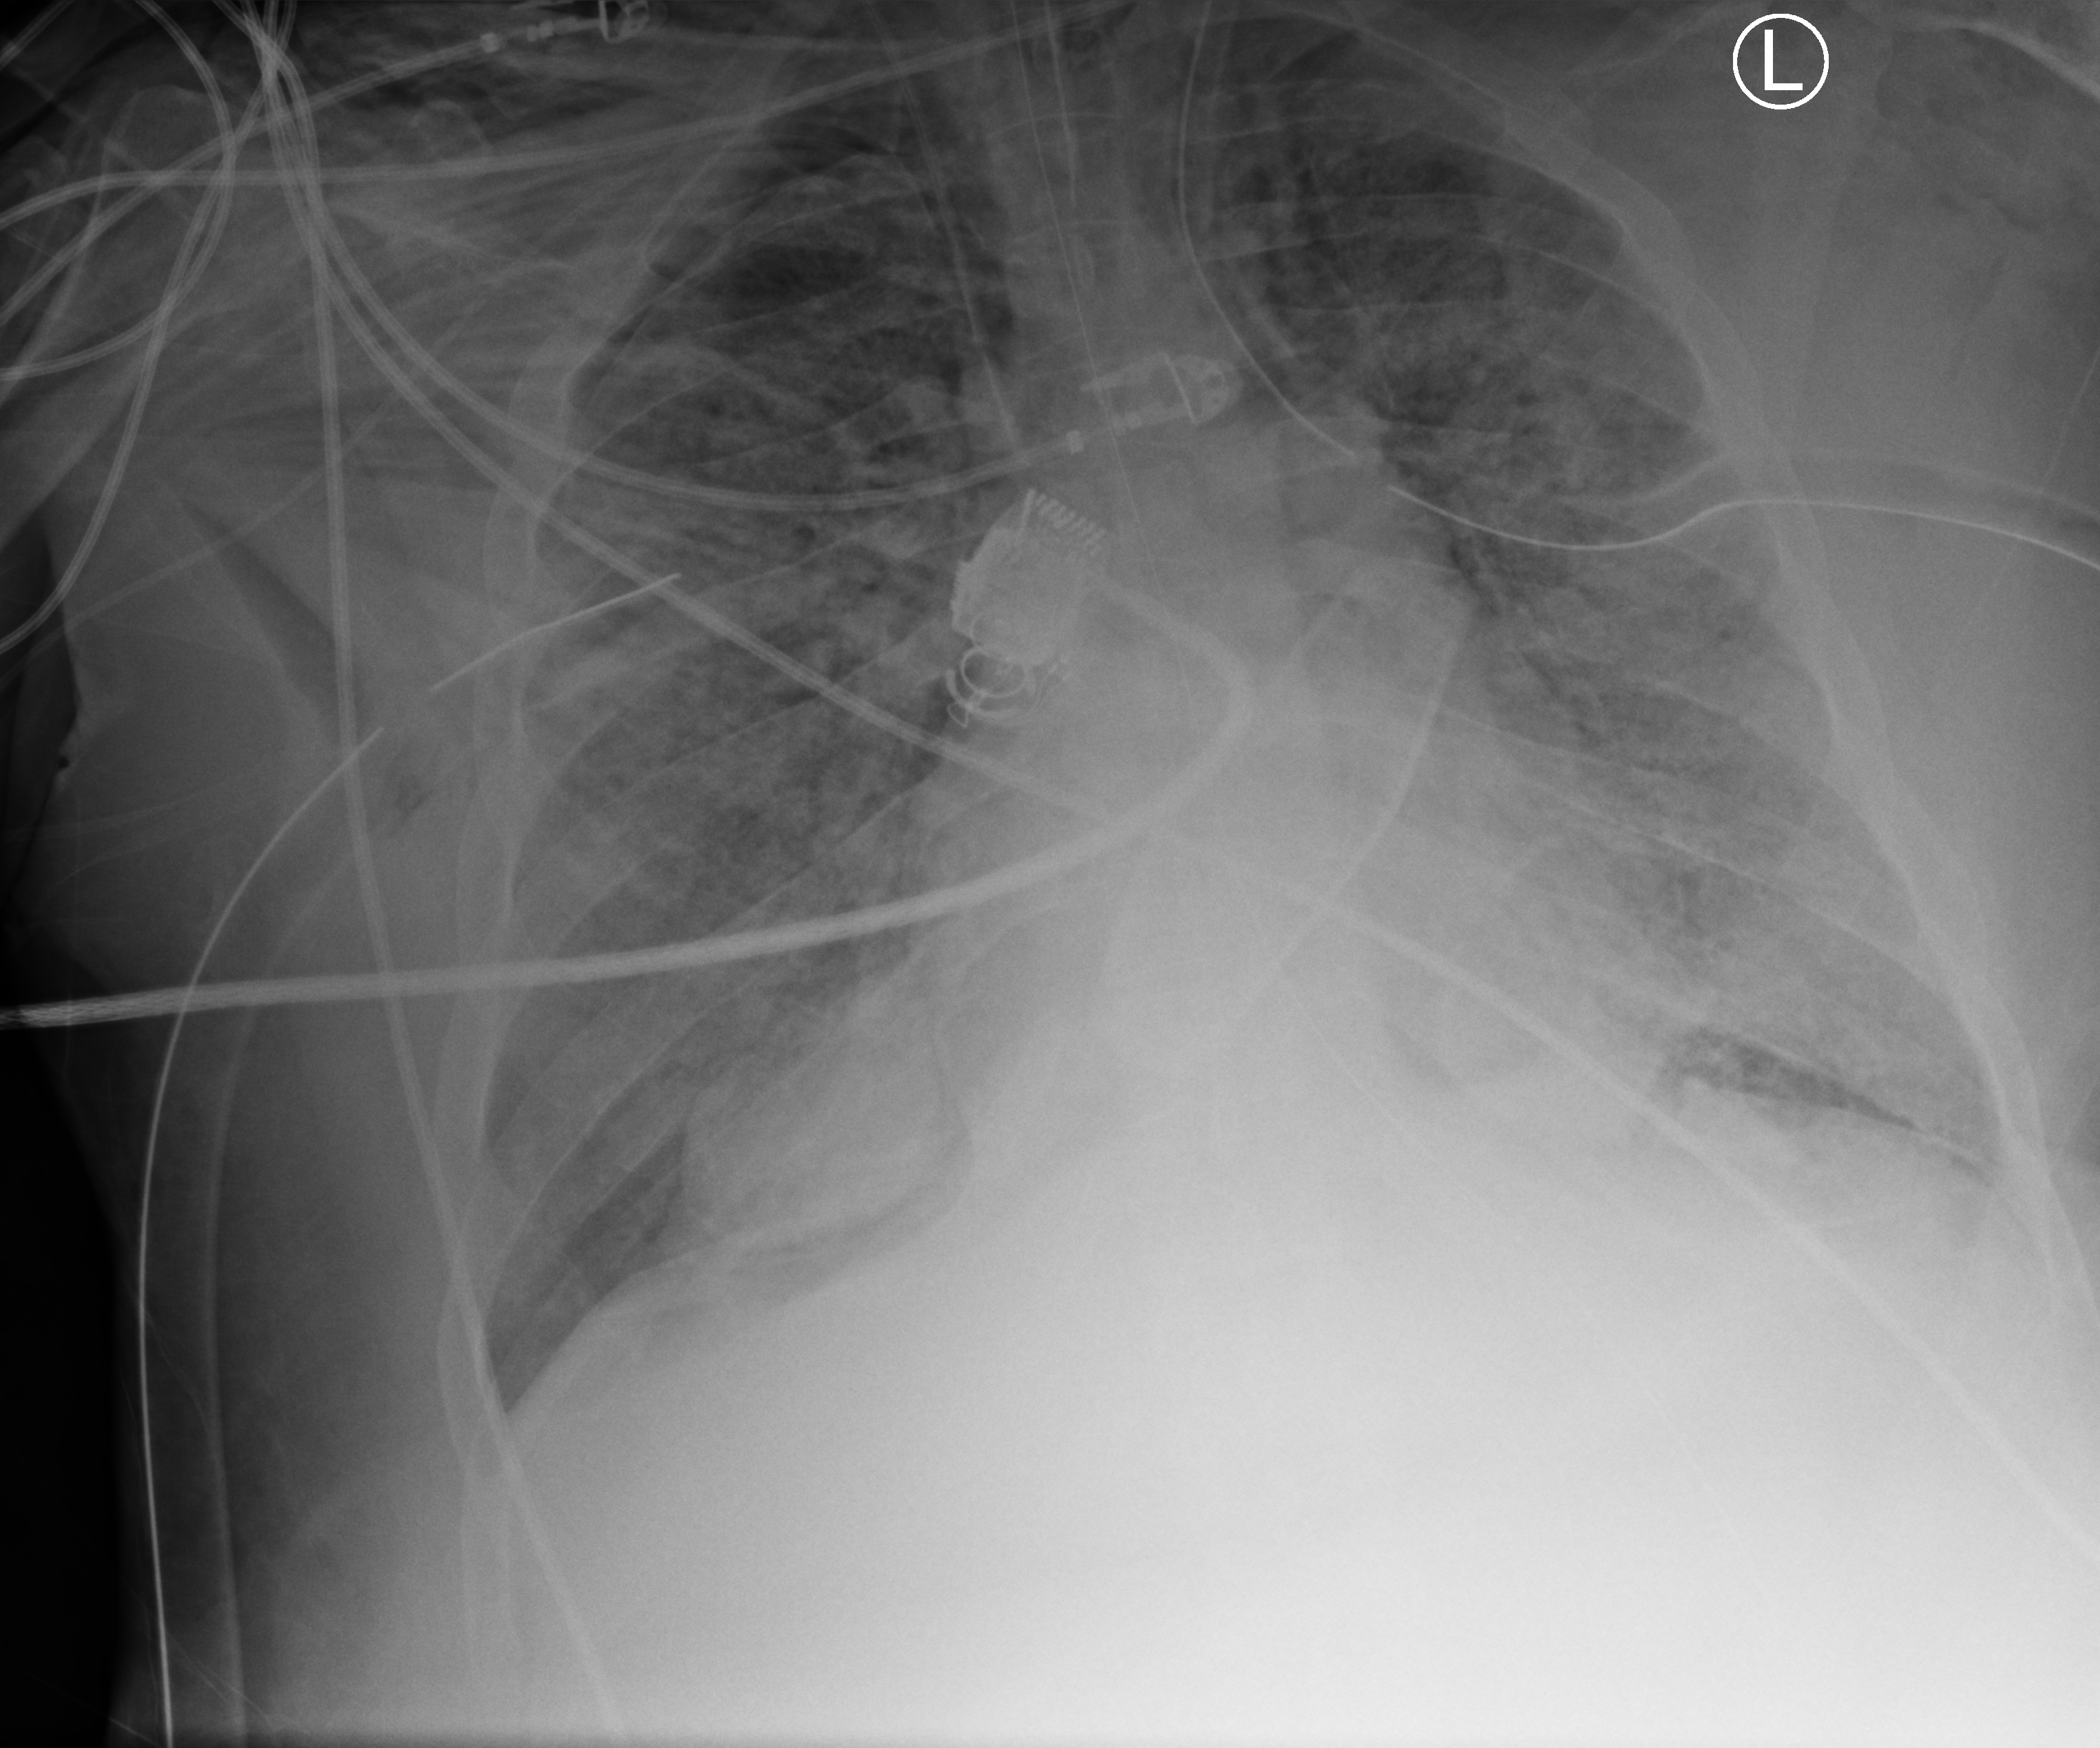
Chest X-ray (portable), anteroposterior (AP) projection. Patient hospitalised with COVID-19, aged 18–59 years.
From the hospital-stay record, not from the radiograph (when in the stay this image was taken is not recorded): chronic kidney disease (admission record): no; admitted to intensive care during this hospital stay: yes; mechanically ventilated during this hospital stay: yes.